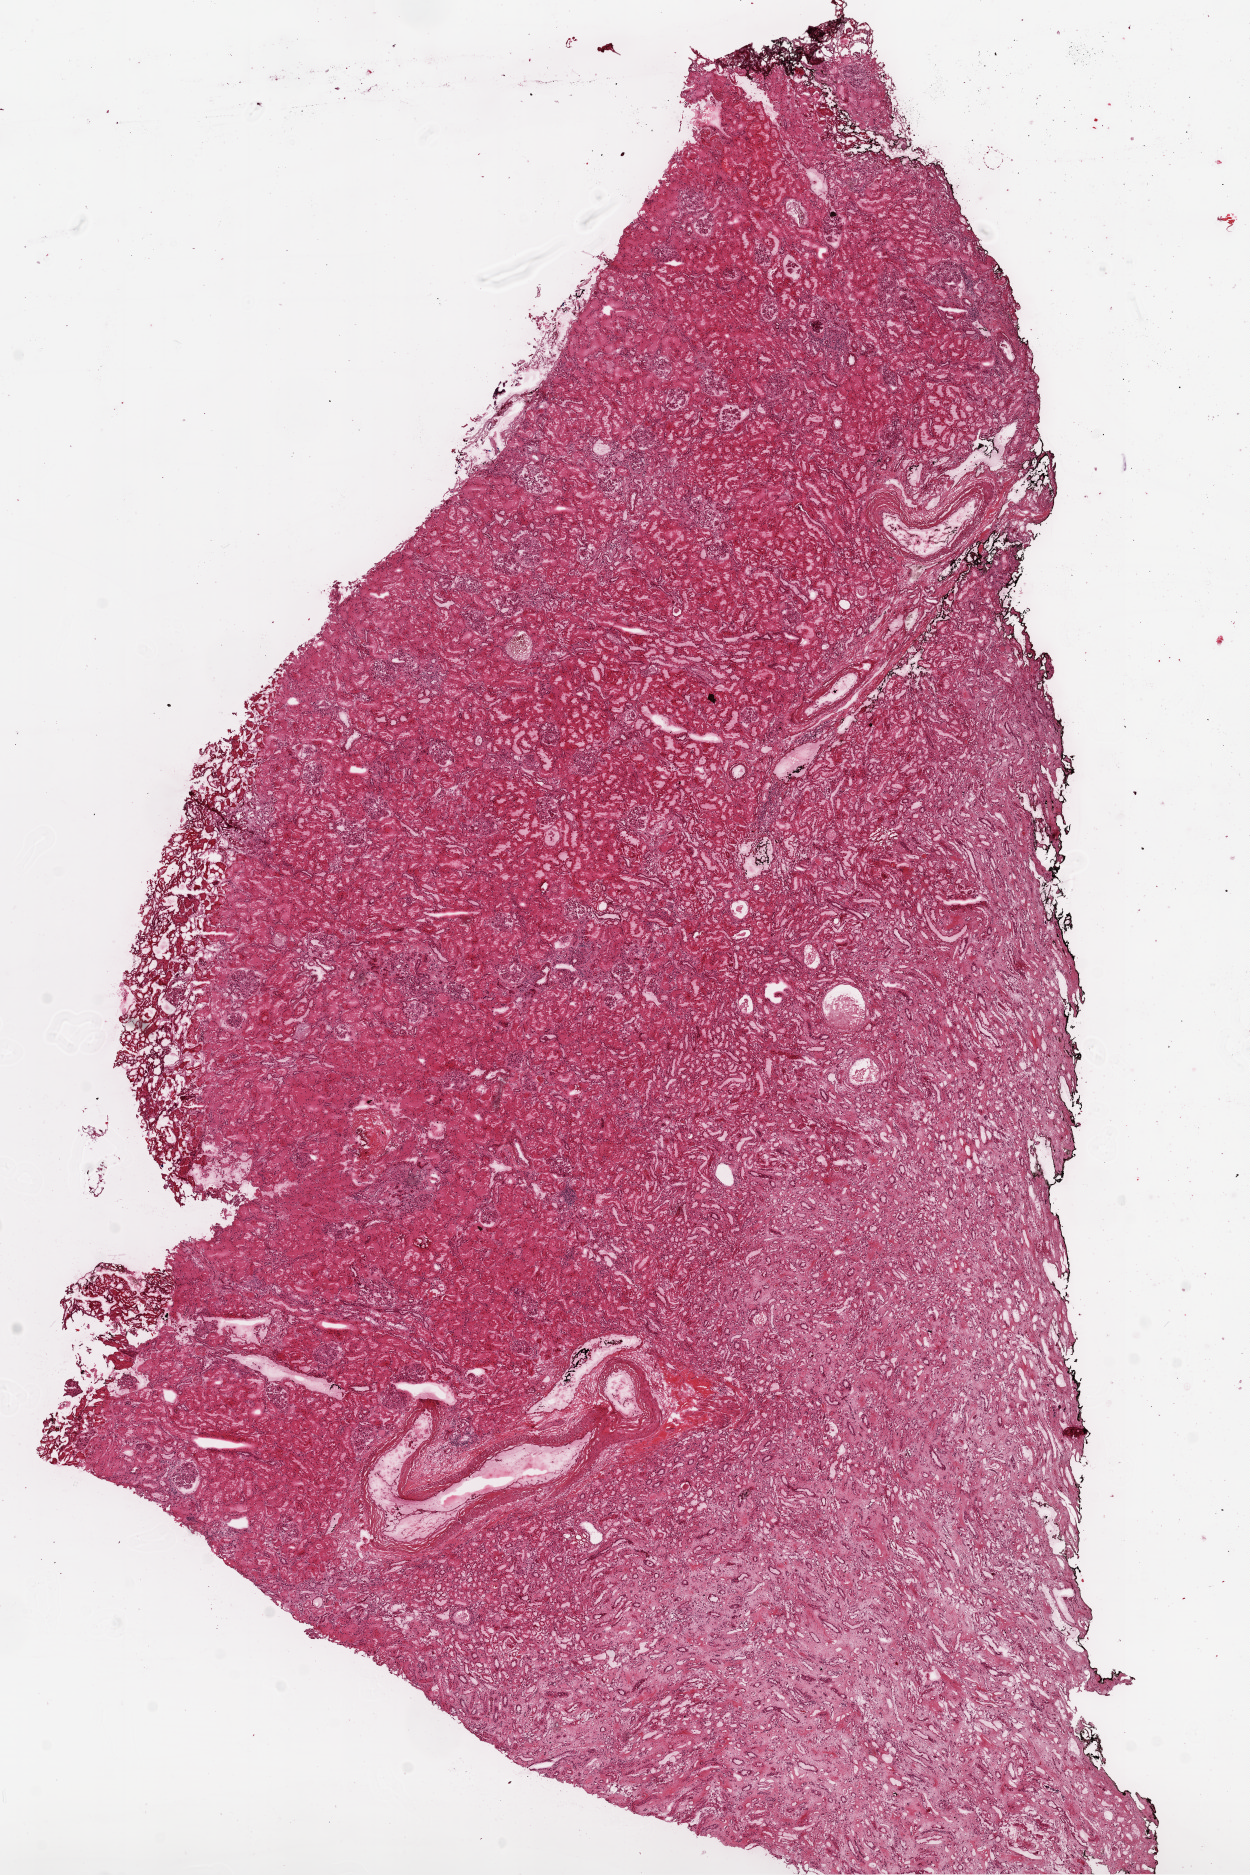
H&E-stained whole-slide image — a low-resolution overview of the entire scanned area, about 10.0 x 15.0 mm; frozen section from the top of the tissue portion; solid tissue normal (non-tumour tissue) sample from the kidney. Female, age 75 years at initial diagnosis.
• this section: solid tissue normal sample (biorepository sample class)
• patient diagnosis: Clear cell adenocarcinoma, NOS